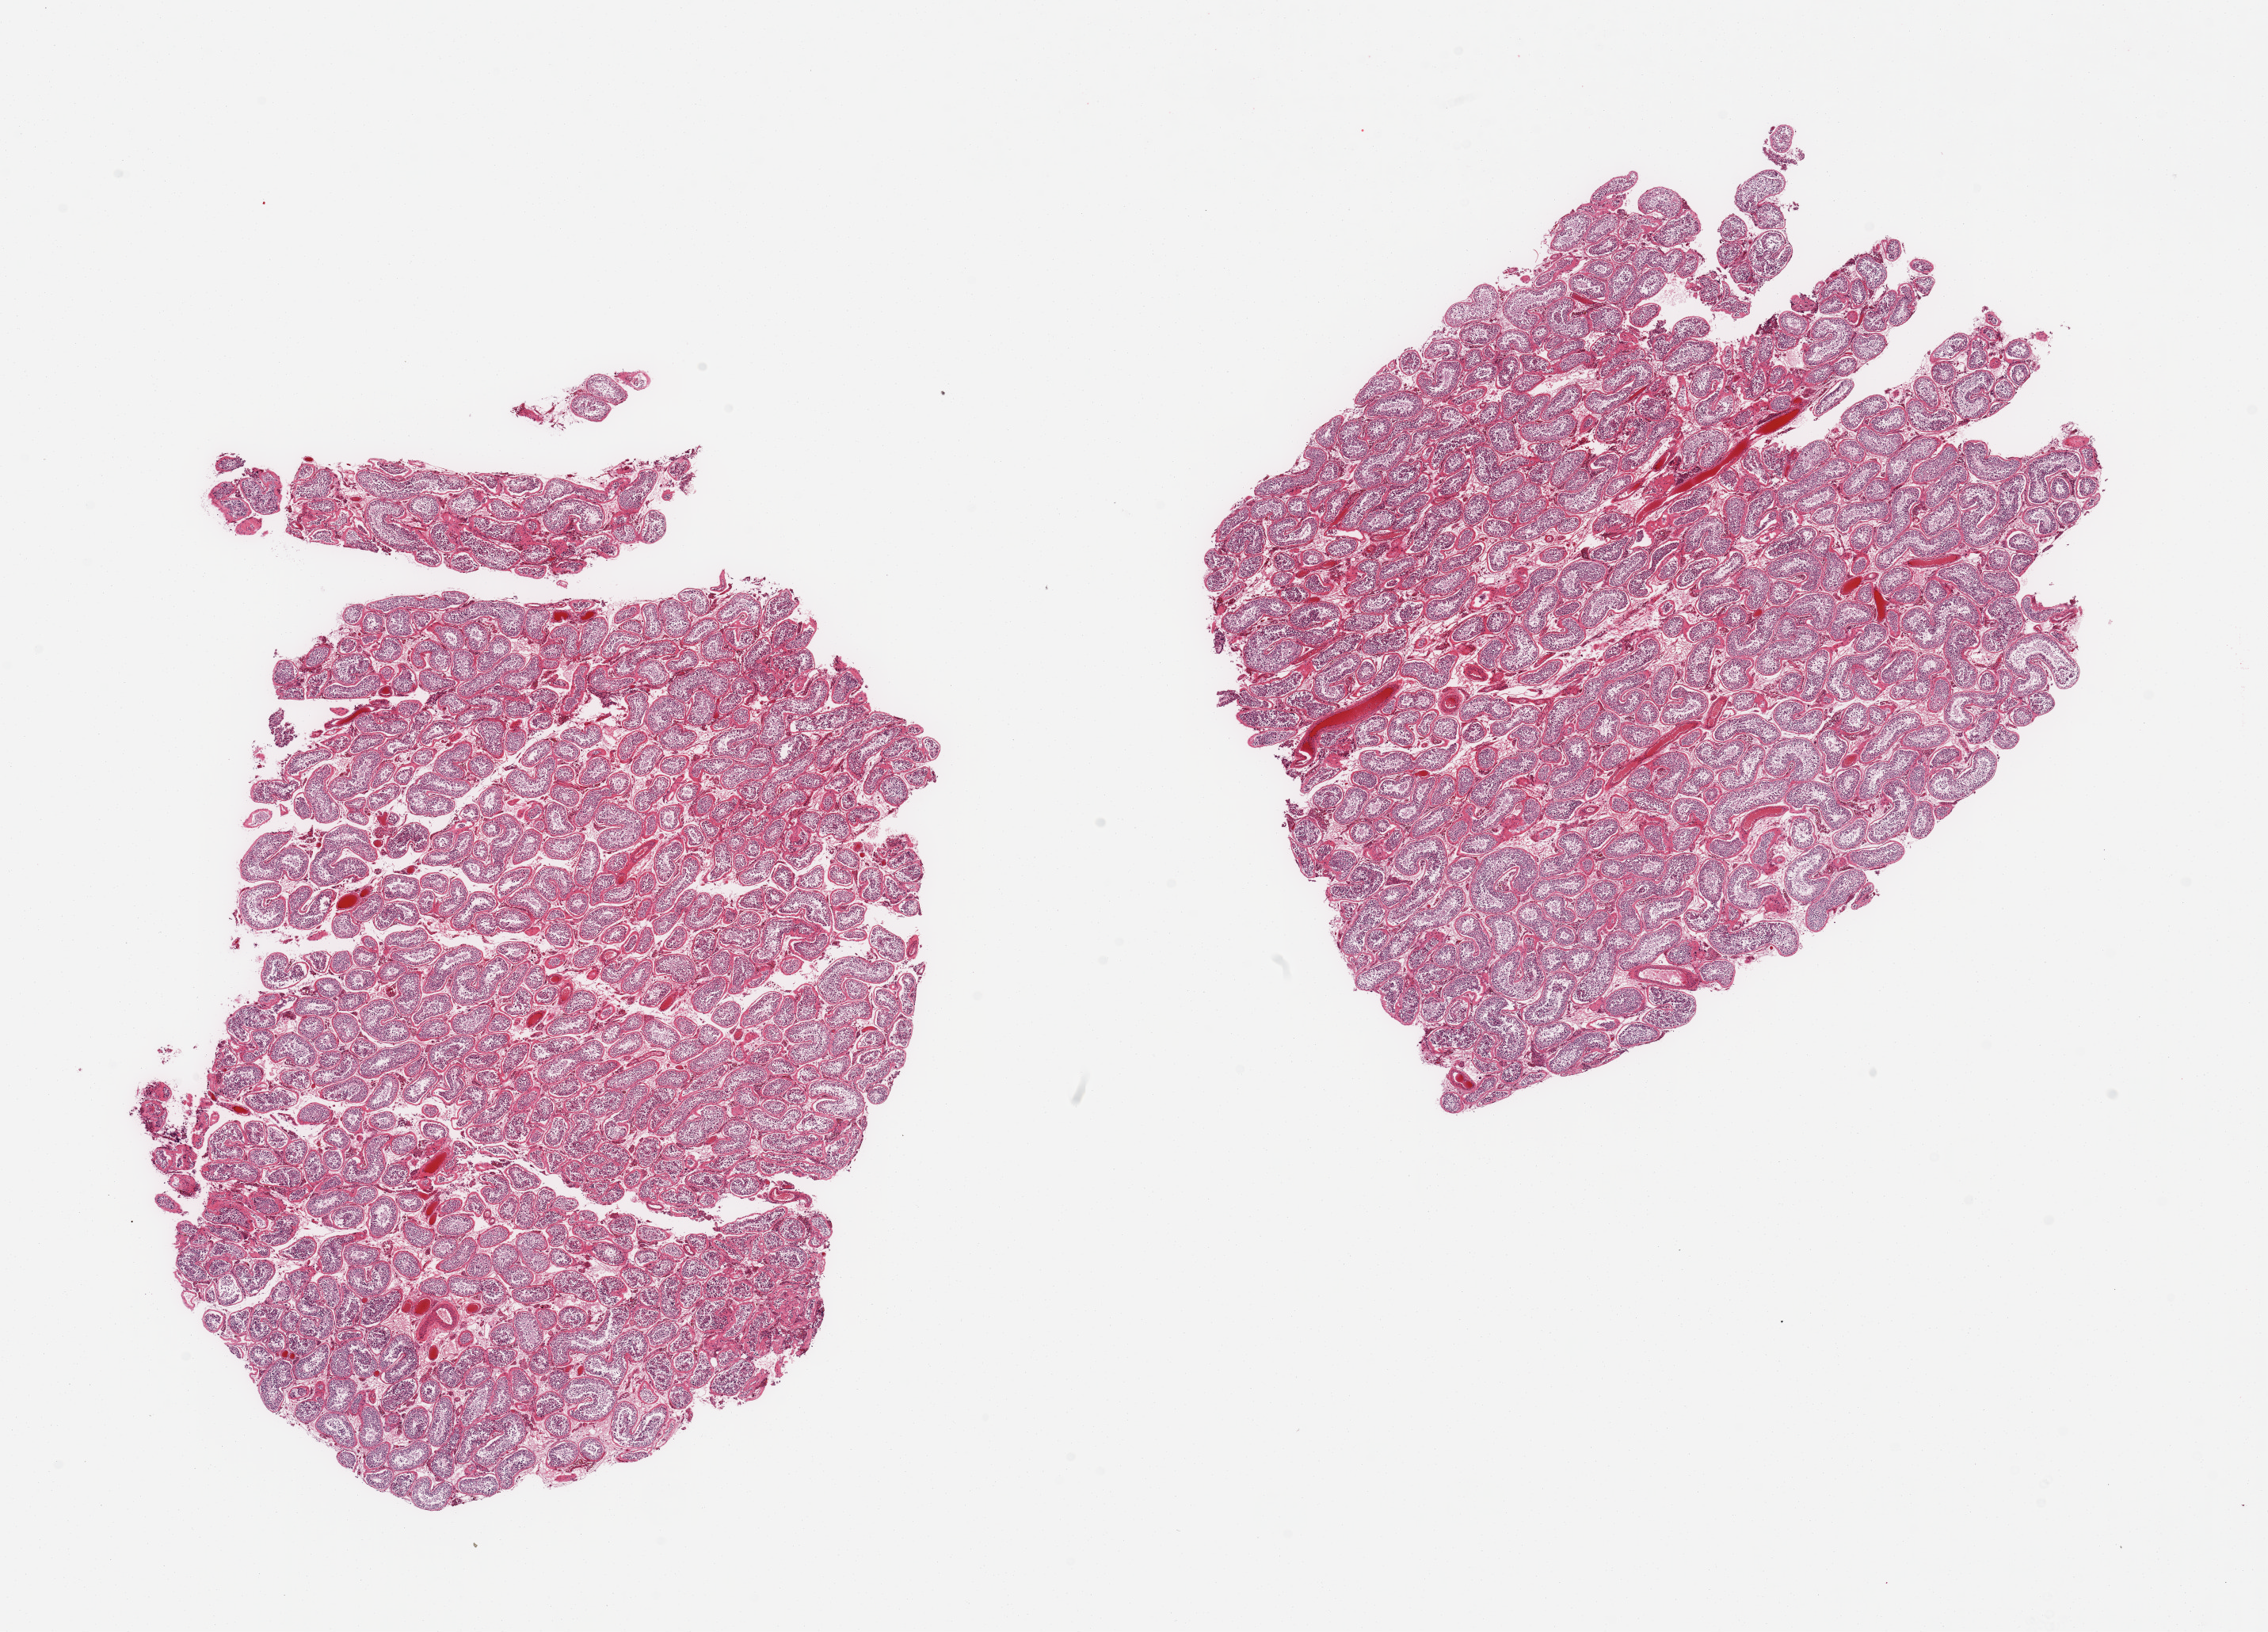
Digitized hematoxylin and eosin (H&E)-stained section — a low-resolution overview of the entire scanned area, about 22.6 x 16.3 mm (acquisition: 20x scan); PAXgene-fixed, paraffin-embedded tissue; section of testis (target tissue); donor tissue sample. Male donor.
Review note (as recorded): 2 pieces; spermatogenesis is present.